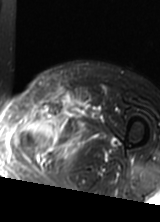
MRI of an extremity soft-tissue mass, one axial slice. Slice 47 of 69 in the series (ordered by position). T2-weighted fat-saturated. MR volume resampled by the dataset authors to the PET/CT grid (not the native acquisition matrix). 160 × 222 image matrix, field of view 156 × 217 mm. Female patient. Case-level facts recorded for this patient, not image findings: histological type: pleomorphic leiomyosarcoma; grade: high; site of the primary tumour: left thigh.
Annotated regions visible in this slice (expert contour drawn on MRI and transferred to this co-registered scan by the dataset authors):
- gross tumour volume including surrounding oedema: box from (x=16, y=91) to (x=87, y=162) px